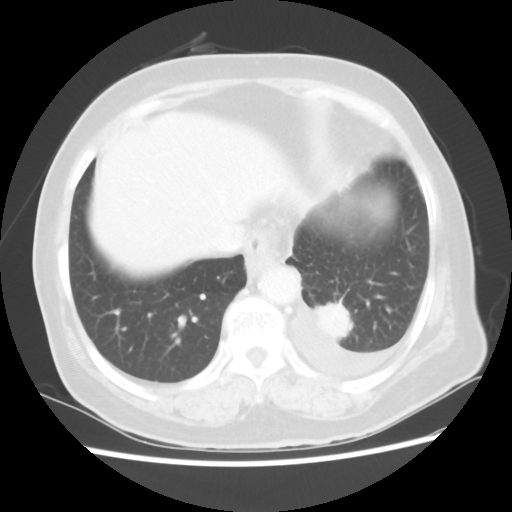
Chest CT, one axial slice. Slice 10 of 80 in the series (ordered by position). Reconstruction kernel STANDARD. 100 kVp. Lung window (W 1500 / L -600 HU). 5 mm slice thickness. 512 × 512 image matrix, field of view 343 × 343 mm. Patient: female, 68 years. From the clinical record (not read from this slice): clinical TNM (as recorded): T1c N0 M1.
Annotated regions visible in this slice (rectangle marked by the reading radiologist):
- lung tumour (recorded histology: adenocarcinoma): box from (x=312, y=298) to (x=359, y=342) px